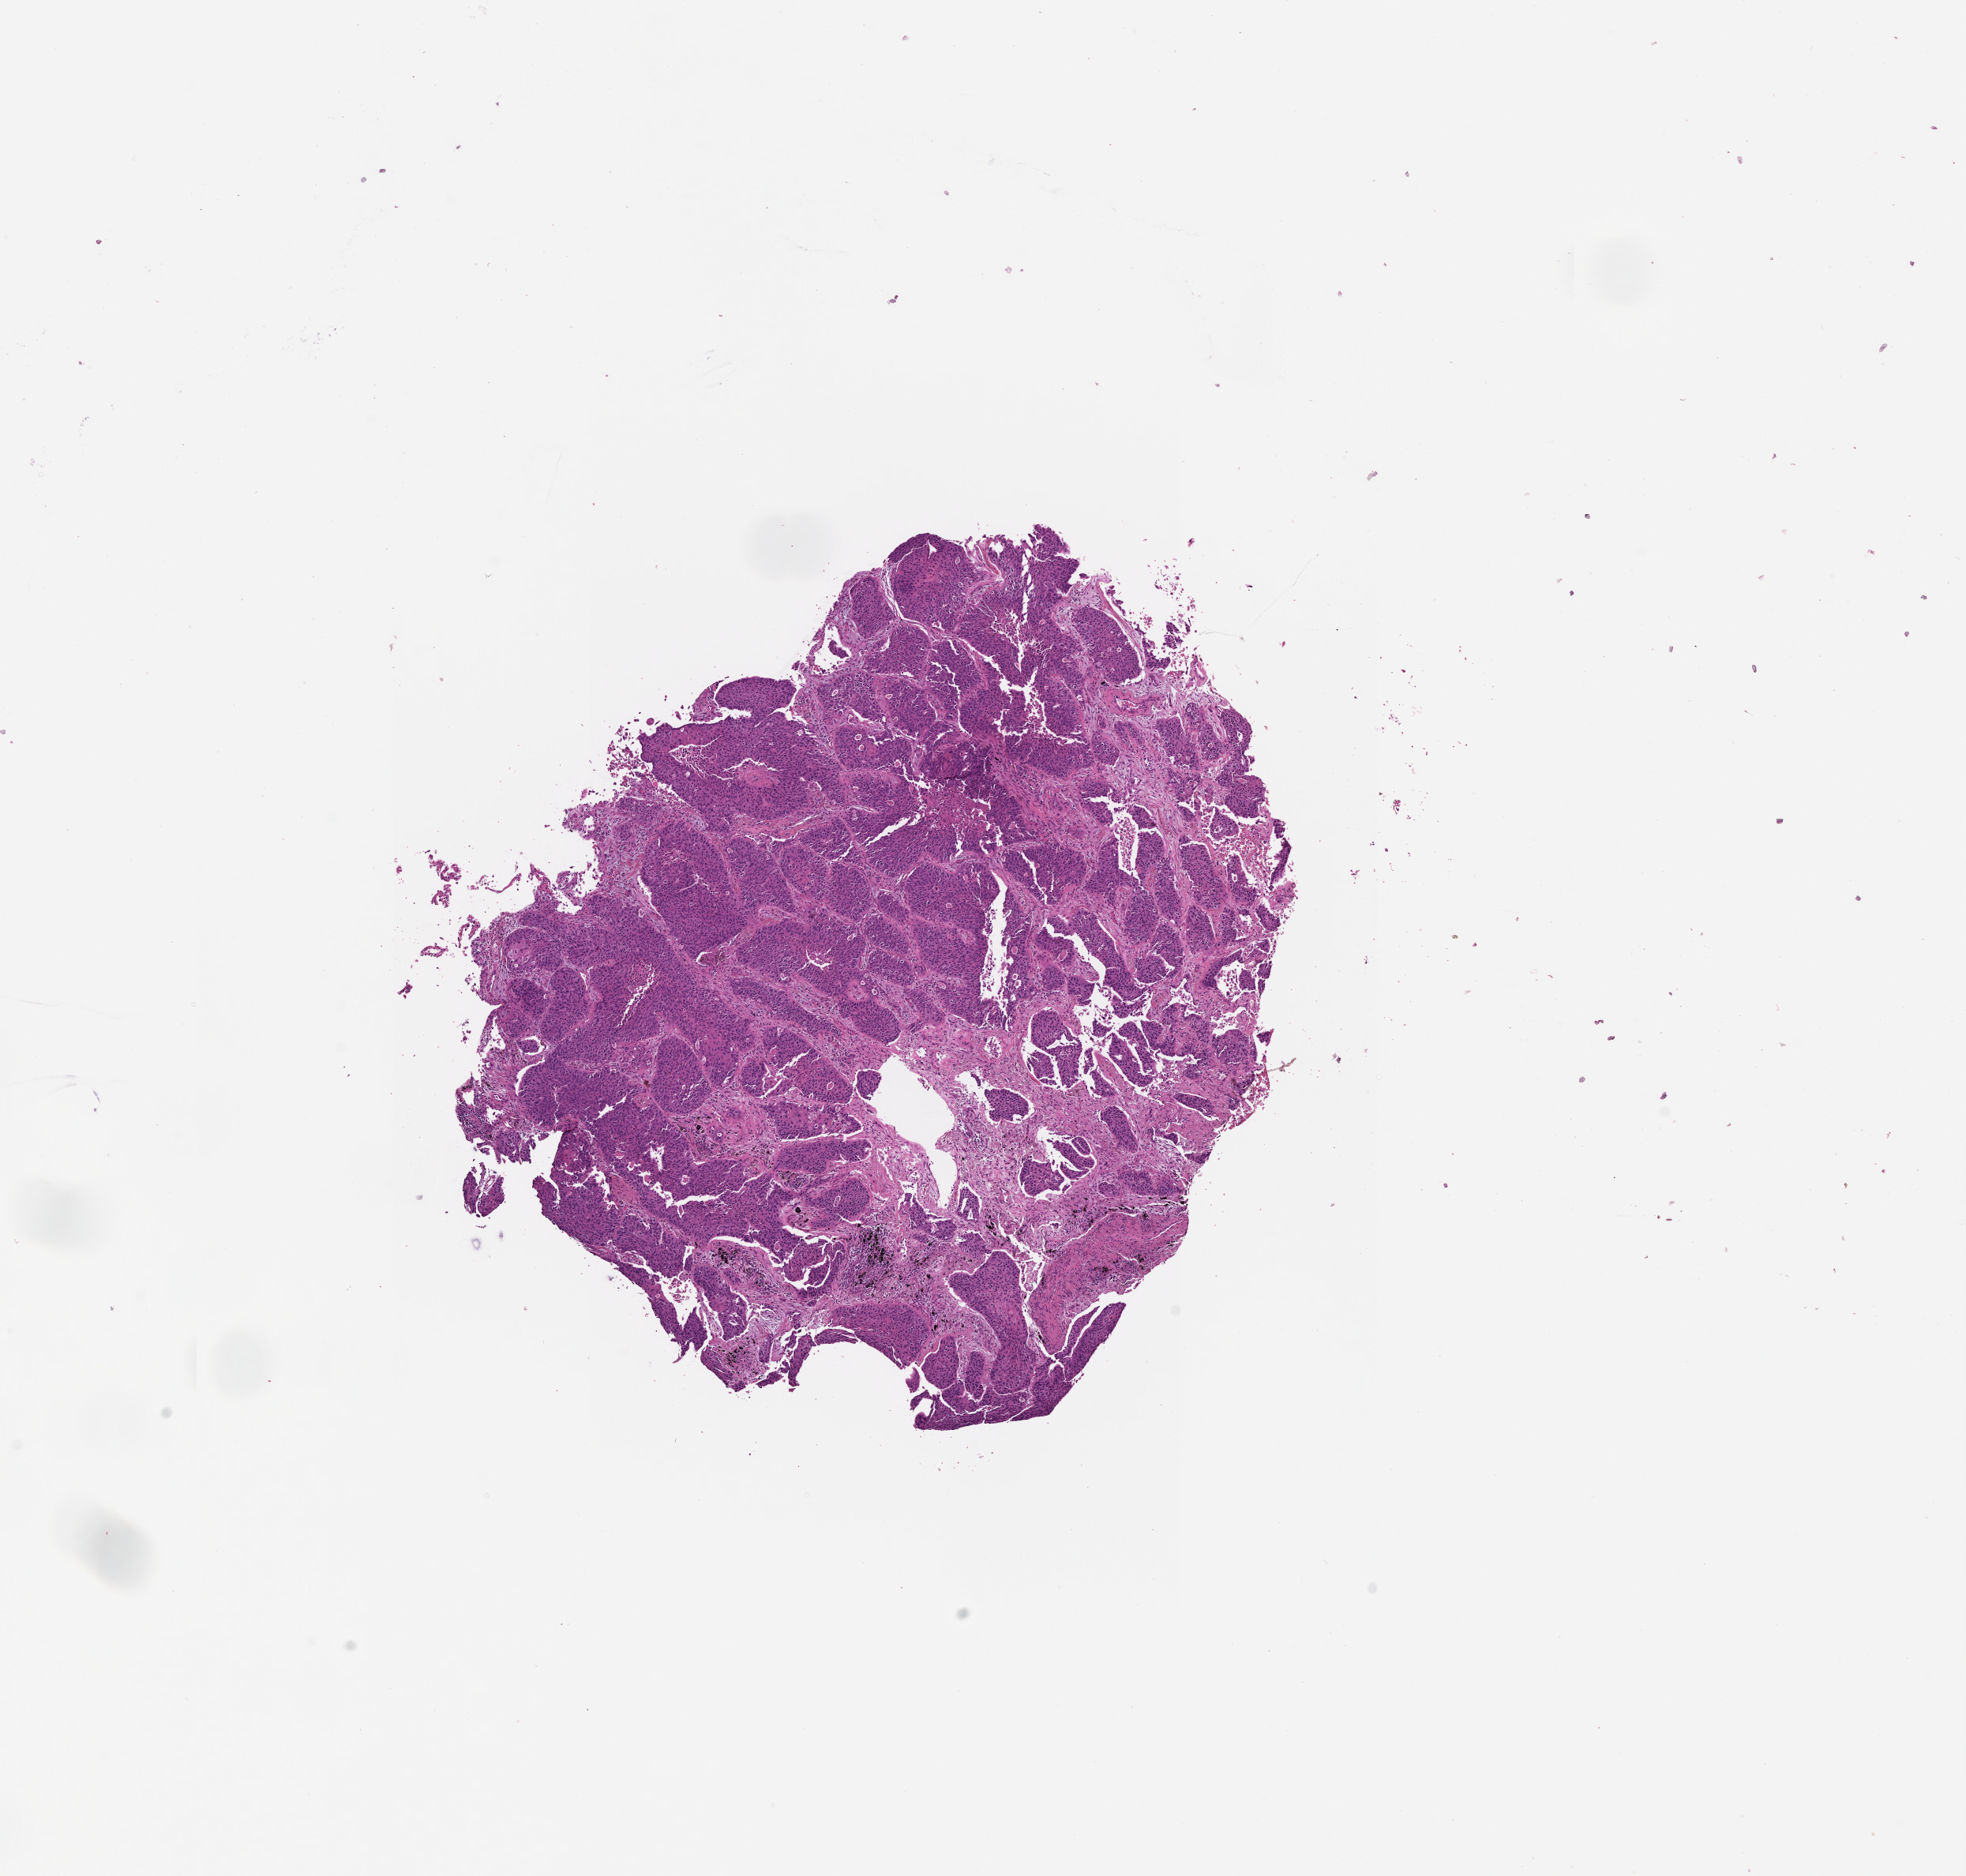
Digitized Hematoxylin and eosin (H&E) stained tissue section (whole slide), low-resolution overview of the scanned area, about 10.0 x 9.6 mm; lung, tissue type not recorded.
- patient diagnosis (cohort enrolment): squamous cell carcinoma (lung)